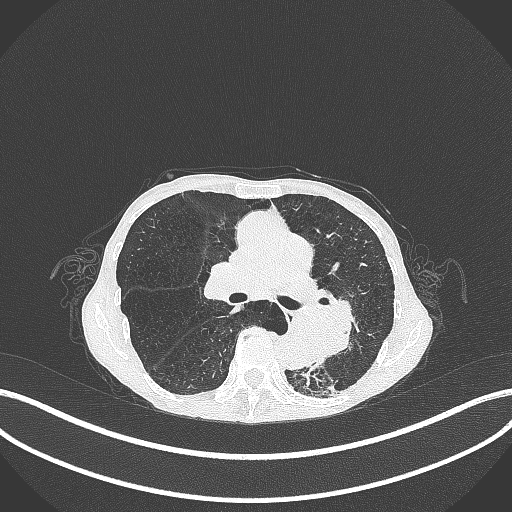
Chest CT, one axial slice. Slice 162 of 347 in the series (ordered by position). 120 kVp. Lung window (W 1500 / L -600 HU). 1 mm slice thickness. 512 × 512 image matrix, field of view 400 × 400 mm. Patient: female, 70 years. Case-level facts recorded for this patient, not image findings: clinical TNM (as recorded): T3 N0 M0.
Structures marked on this image (rectangle marked by the reading radiologist):
- lung tumour (recorded histology: small cell carcinoma): bounding box (x1, y1, x2, y2) in pixels: (284, 300, 360, 358)